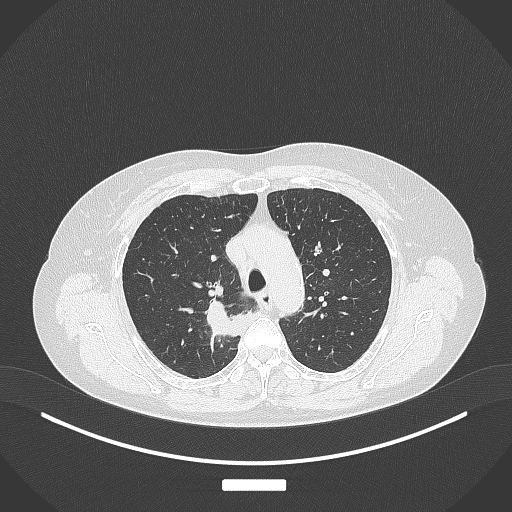
Chest CT, one axial slice; slice 282 of 357 in the series (ordered by position); reconstruction kernel B70f; lung window (W 1500 / L -600 HU); 512 × 512 image matrix, field of view 400 × 400 mm. Female patient, age 62 years. From the clinical record (not read from this slice): clinical TNM (as recorded): T1c N1 M0.
Annotated regions visible in this slice (bounding box drawn by a radiologist):
- lung tumour (recorded histology: squamous cell carcinoma): bounding box (x1, y1, x2, y2) in pixels: (204, 293, 248, 346)